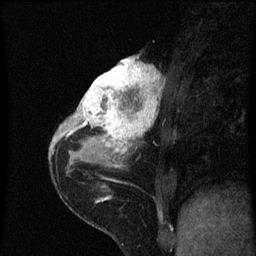
Breast MRI (dynamic contrast-enhanced), one sagittal slice; position 26 of 60 along the scan axis; dynamic contrast-enhanced series, image 2 of 3 at this slice position (ordered by acquisition); 1.5 T; TE 4.2 ms, TR 8 ms; 2 mm slice thickness; 256 × 256 image matrix. Patient: female, 38 years.
Structures marked on this image (semi-automatically segmented with operator editing):
- analysis volume of interest (the breast-tissue region the enhancement analysis was run in; not a lesion): bounding box (x1, y1, x2, y2) in pixels: (80, 56, 163, 151)
- tumour enhancement mask (voxels above the 70 % enhancement threshold inside the analysis volume of interest): (80, 56, 161, 151)